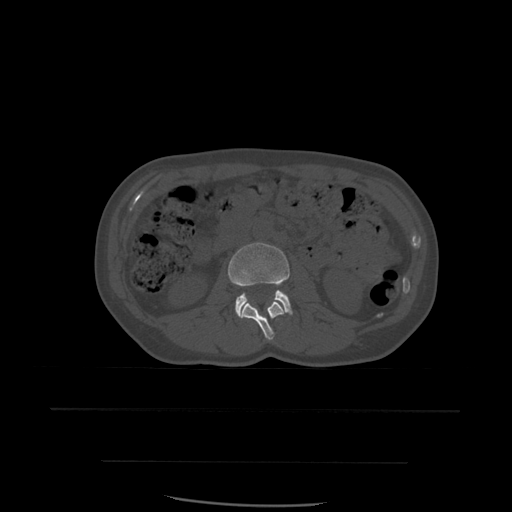
CT including the spine, one axial slice; bone window (W 1800 / L 400 HU); 1.25 mm slice thickness; 512 × 512 image matrix, field of view 392 × 392 mm. Patient age 48 years. From the clinical record (not read from this slice): primary cancer: lung; vertebrae with lytic lesions (as recorded): T11.
Outlined on this slice (semi-automatic segmentation, software-assisted and operator-edited):
- L2 vertebra: bounding box [x1, y1, x2, y2] px = [240, 302, 284, 341]
- L3 vertebra: [228, 242, 293, 317]